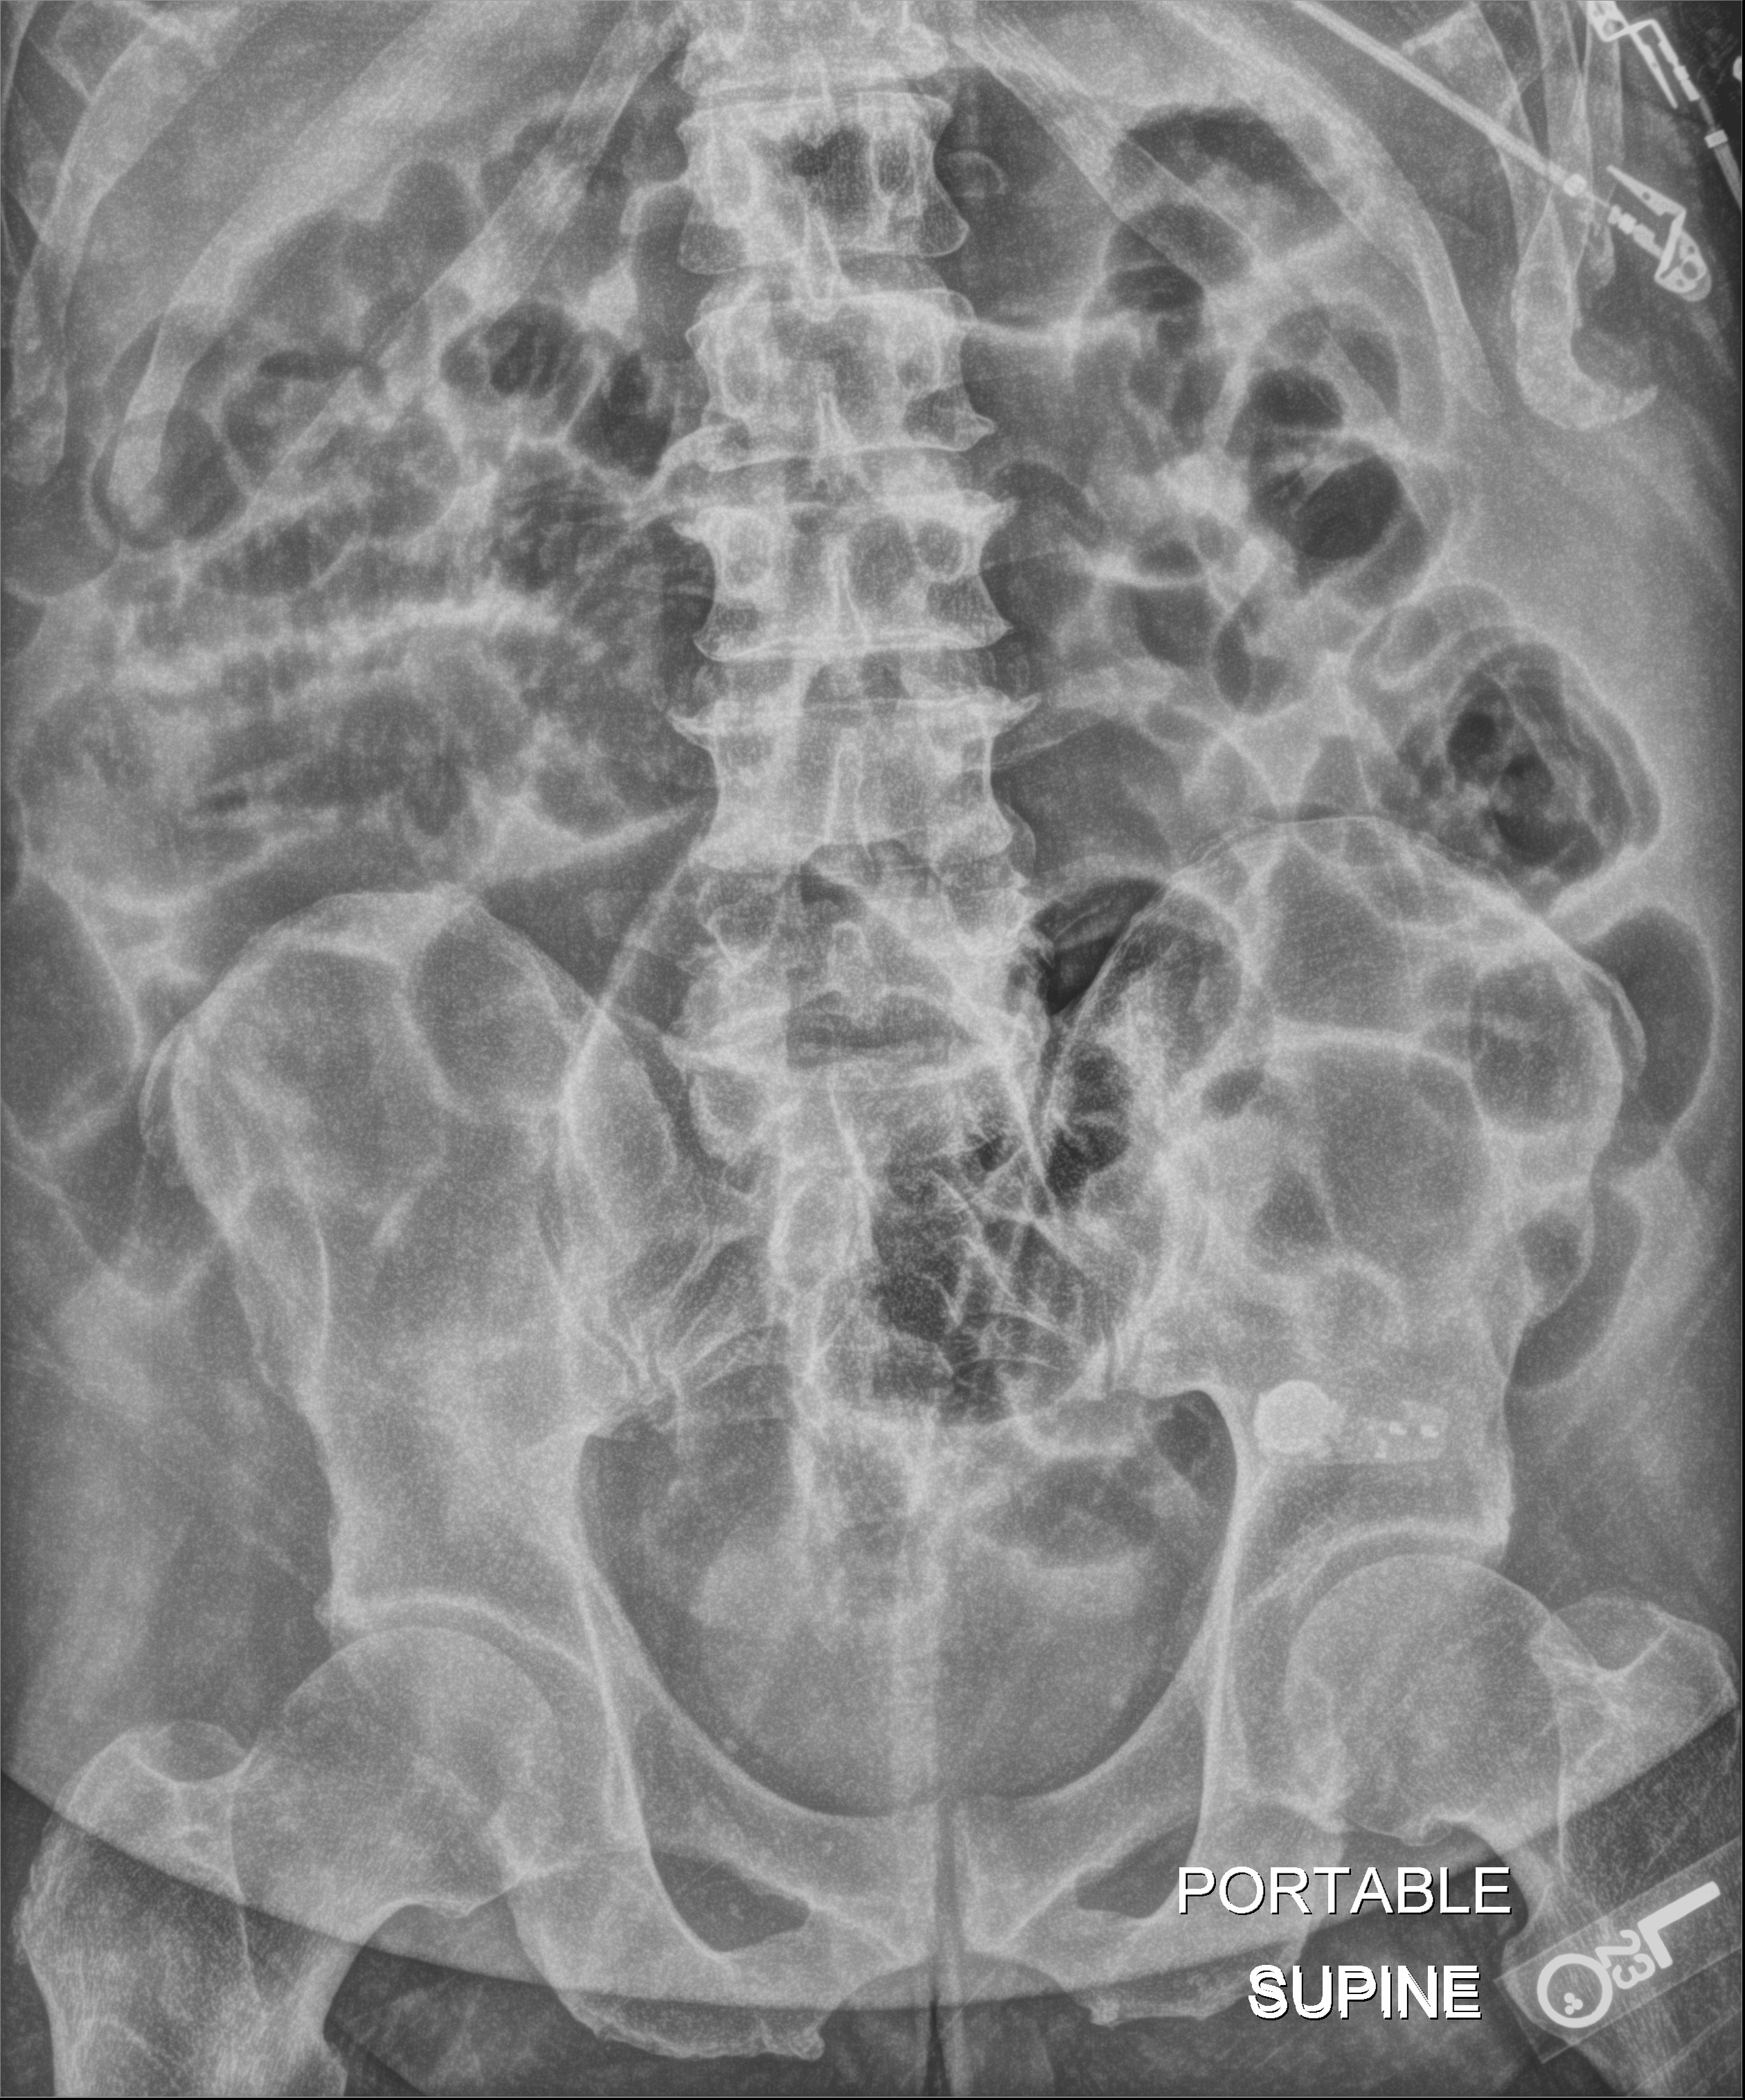
Abdomen X-ray (portable); anteroposterior (AP) projection. Male patient hospitalised with COVID-19, age 18–59 years.
Hospital-stay facts (about this admission, not read from this image; timing relative to this image not recorded): admitted to intensive care during this hospital stay: yes.